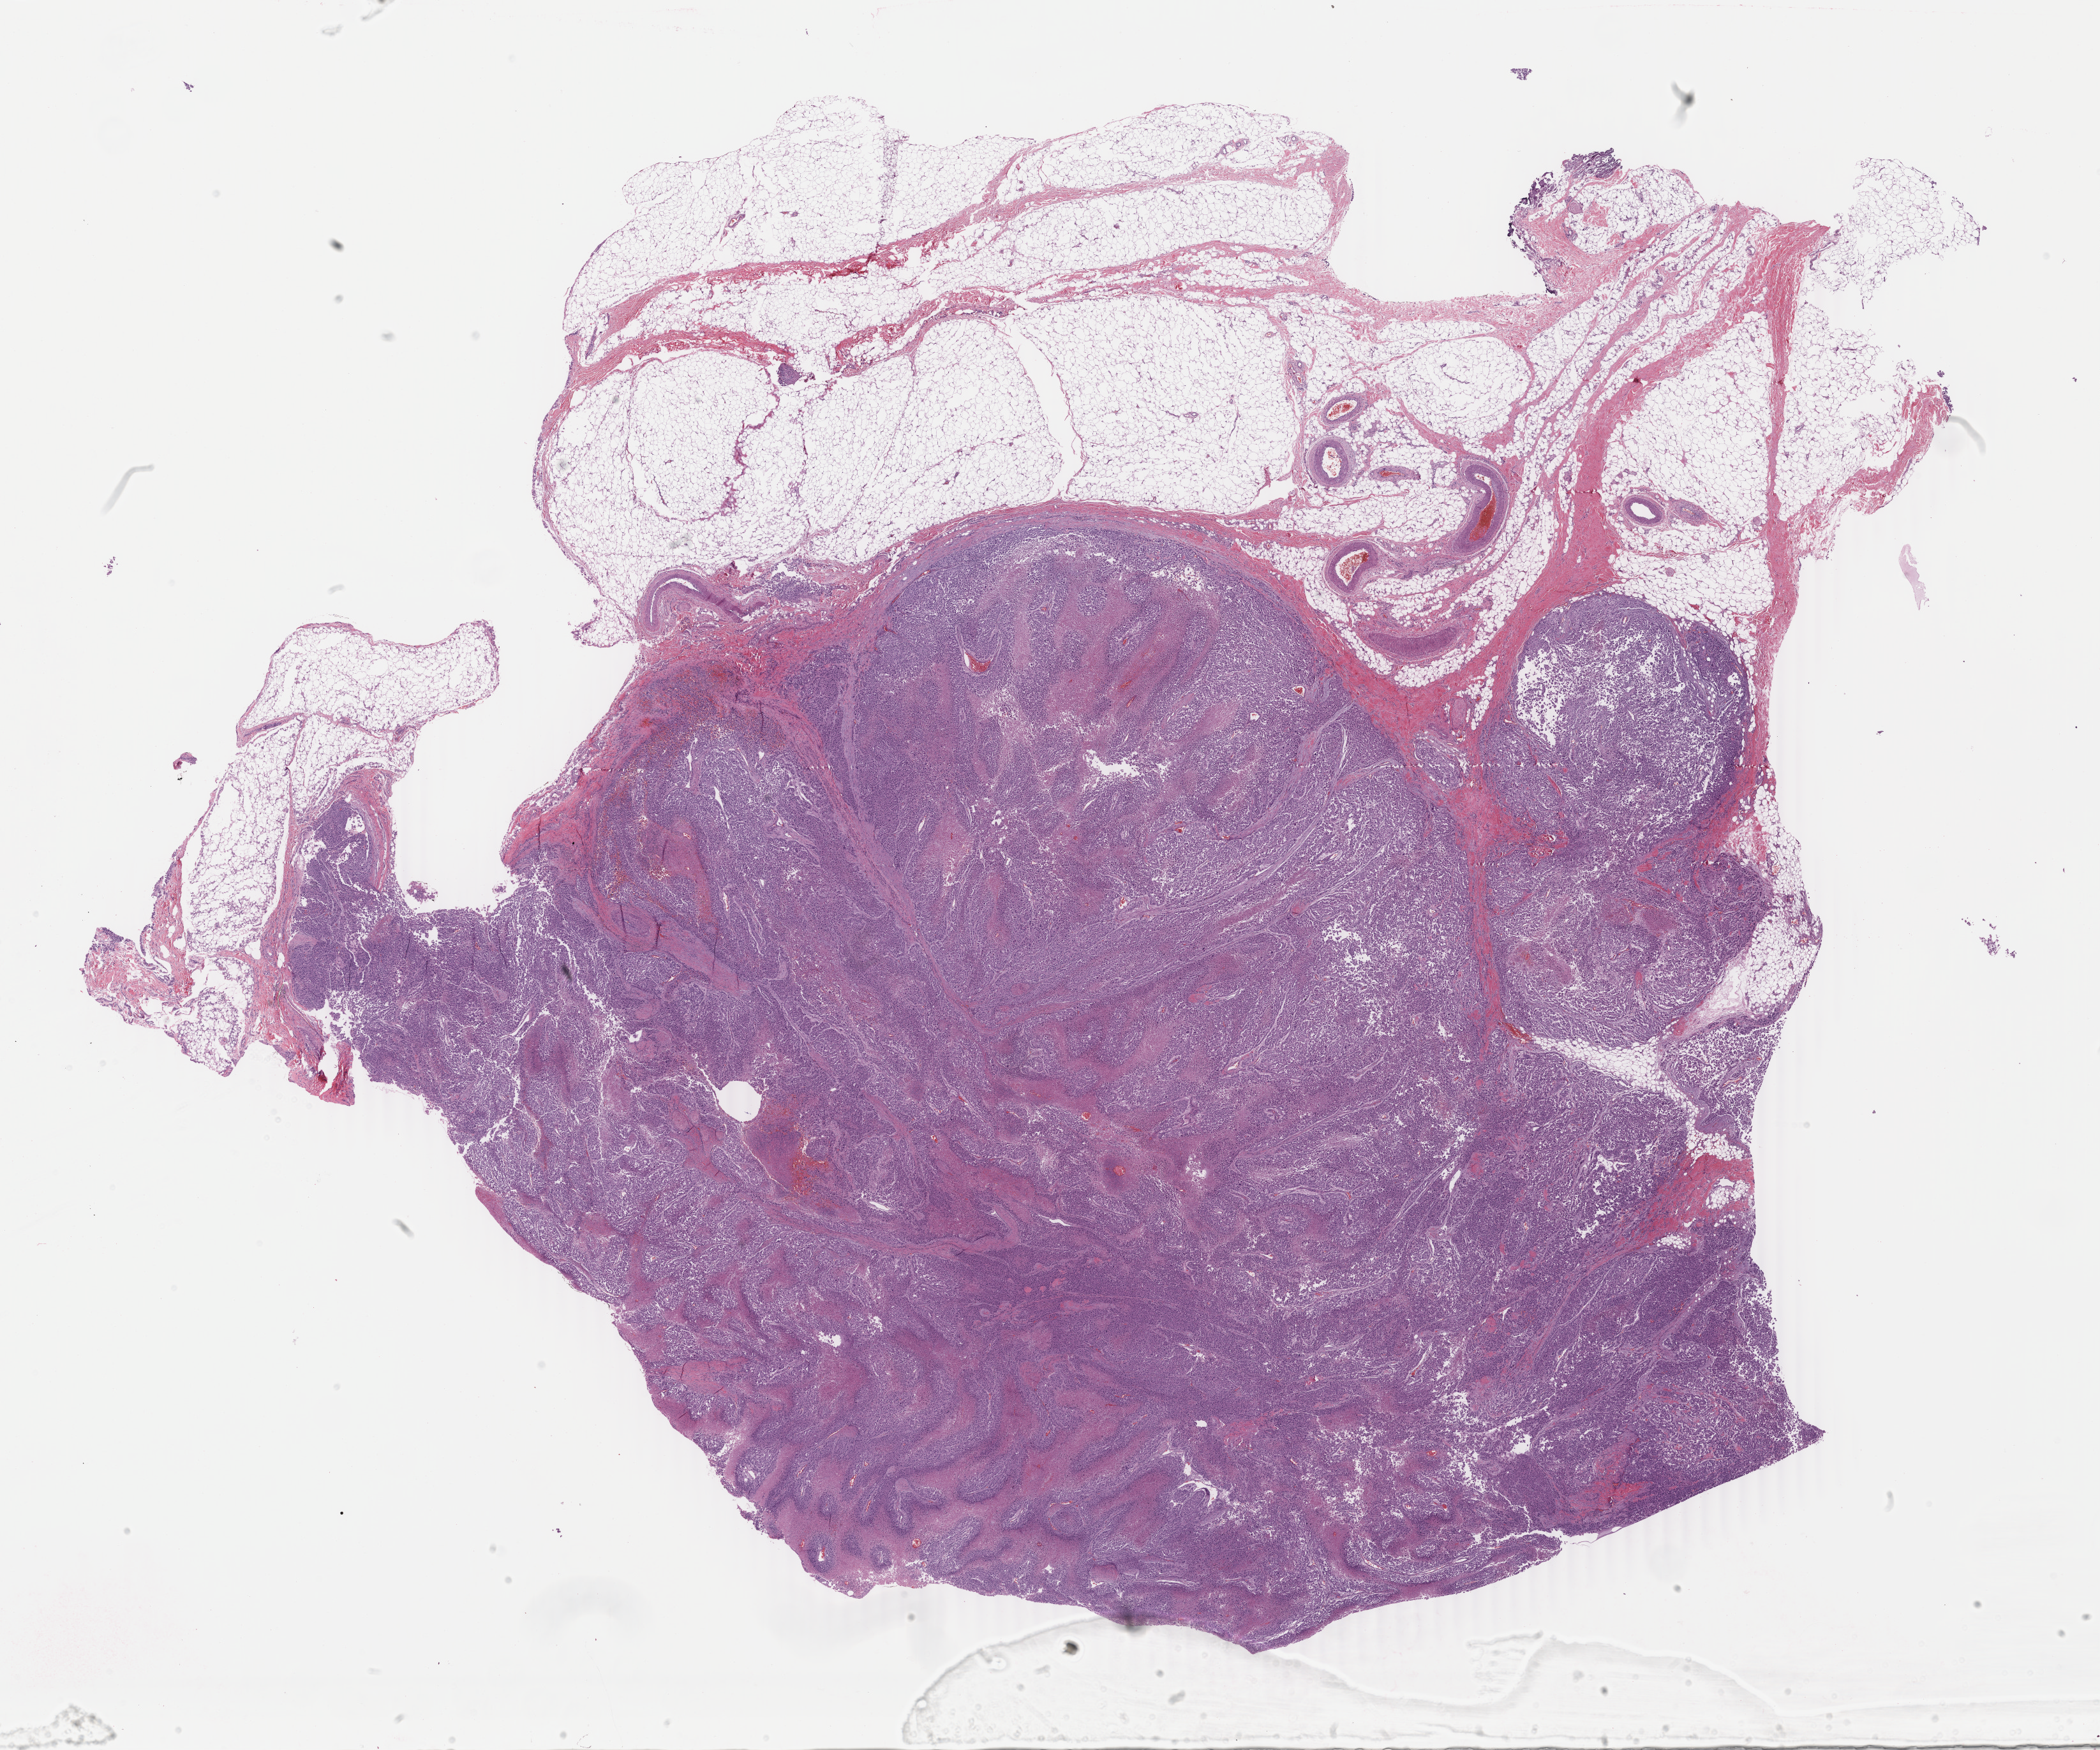
Whole-slide histology image, Hematoxylin and eosin (H&E) stained — low-resolution overview of the scanned area, about 26.2 x 21.8 mm; formalin-fixed paraffin-embedded (FFPE) diagnostic section; skin, primary tumour sample. Male, age 42 years at initial diagnosis.
Pathologic diagnosis: Malignant melanoma, NOS.